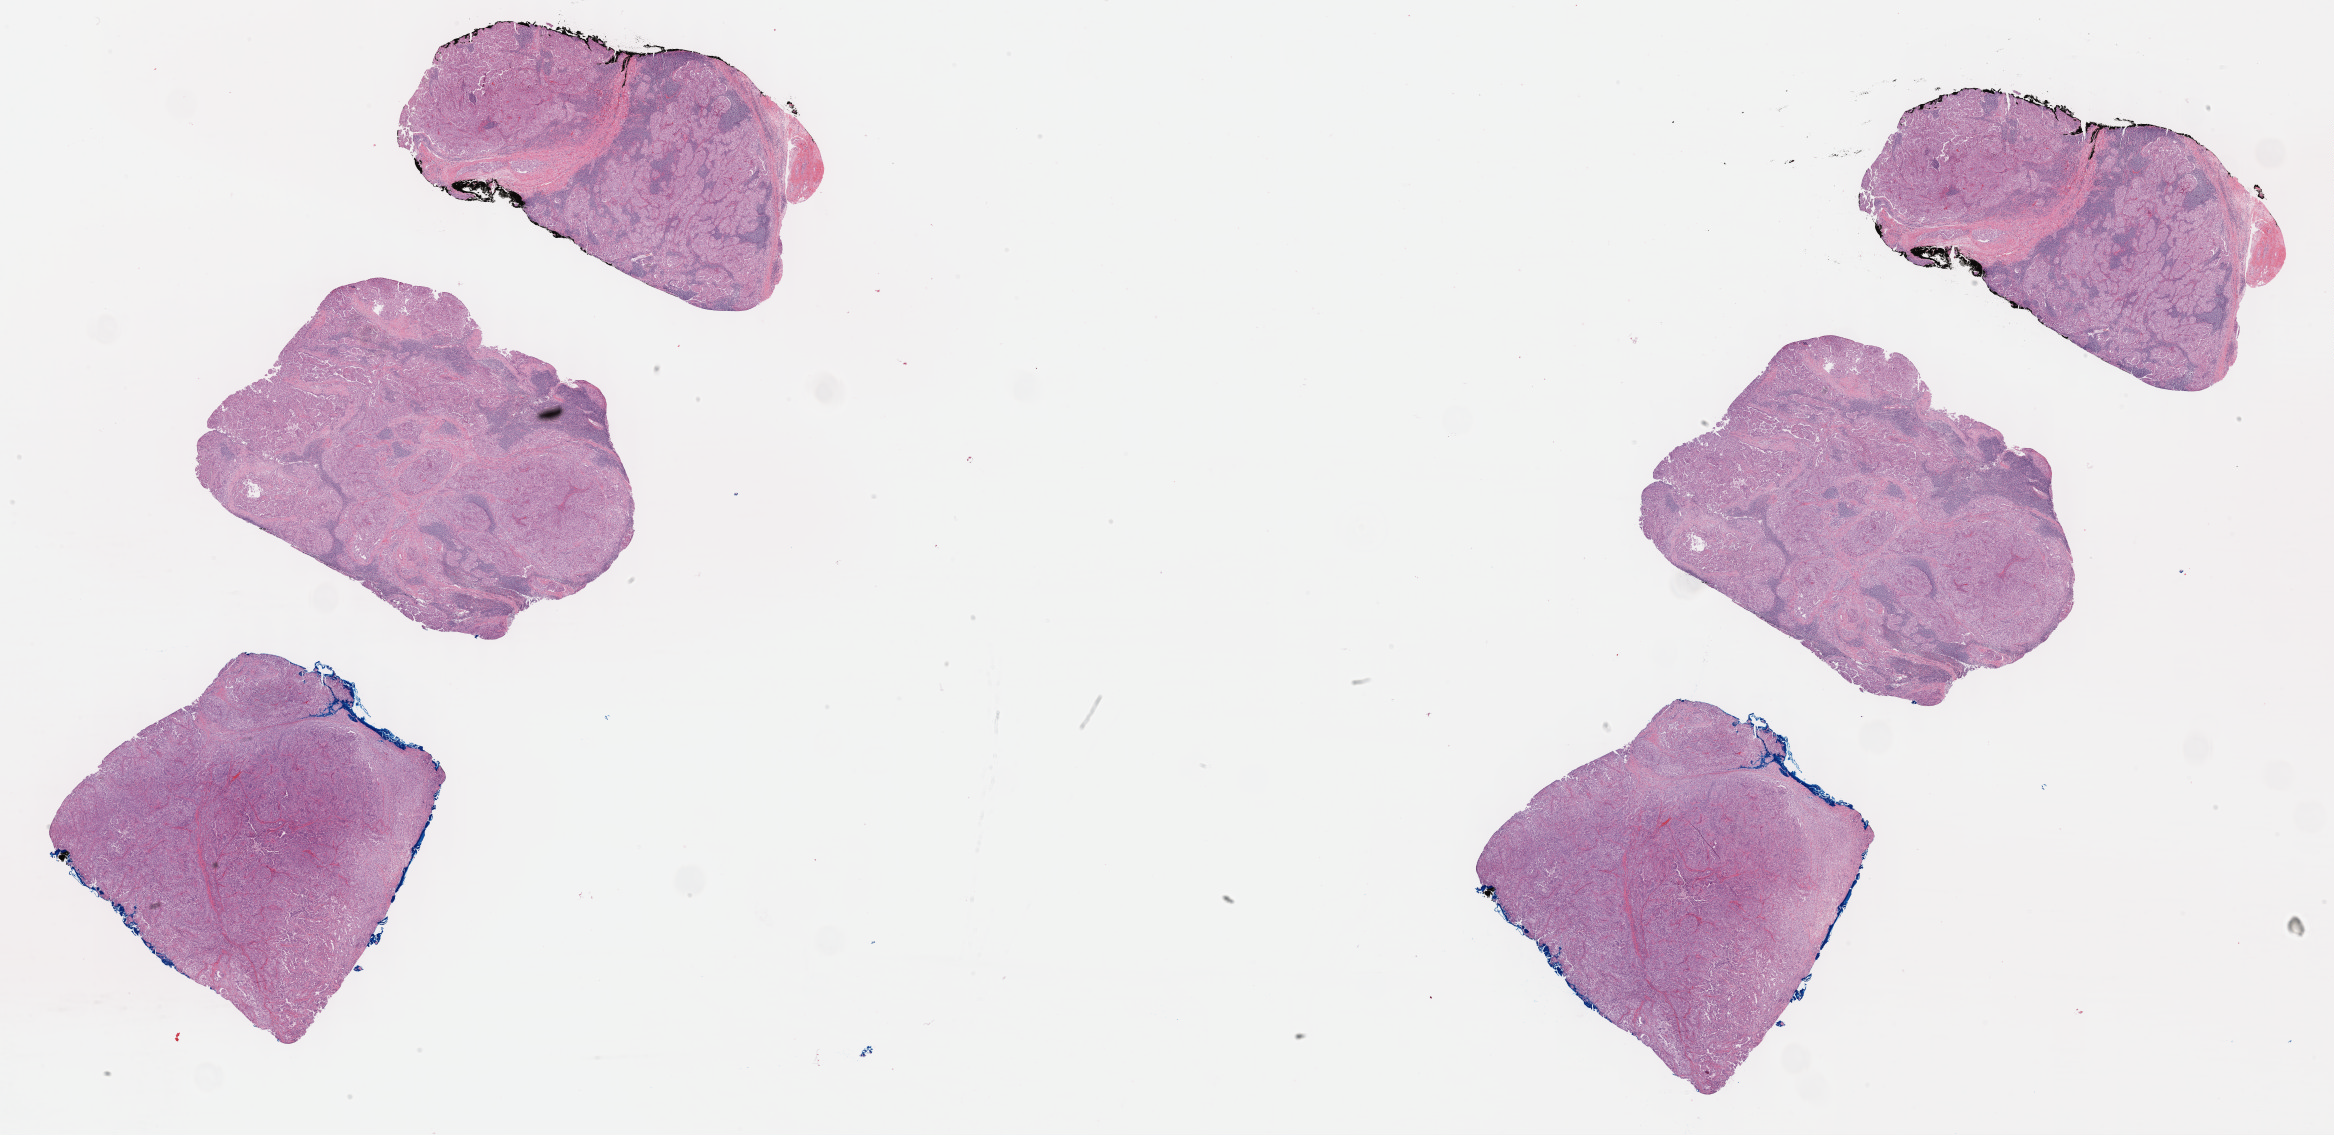
Whole-slide histology image, H&E, whole scanned area (about 37.8 x 18.4 mm, slide scanned at 40x) shown as a low-resolution overview. Formalin-fixed paraffin-embedded (FFPE) diagnostic section. Kidney, primary tumour sample. Male patient; age at initial diagnosis 60 years.
• AJCC pathologic stage: IV (7th edition)
• lymph nodes positive (case pathology): 1 of 2 examined
• diagnosis: Papillary adenocarcinoma, NOS